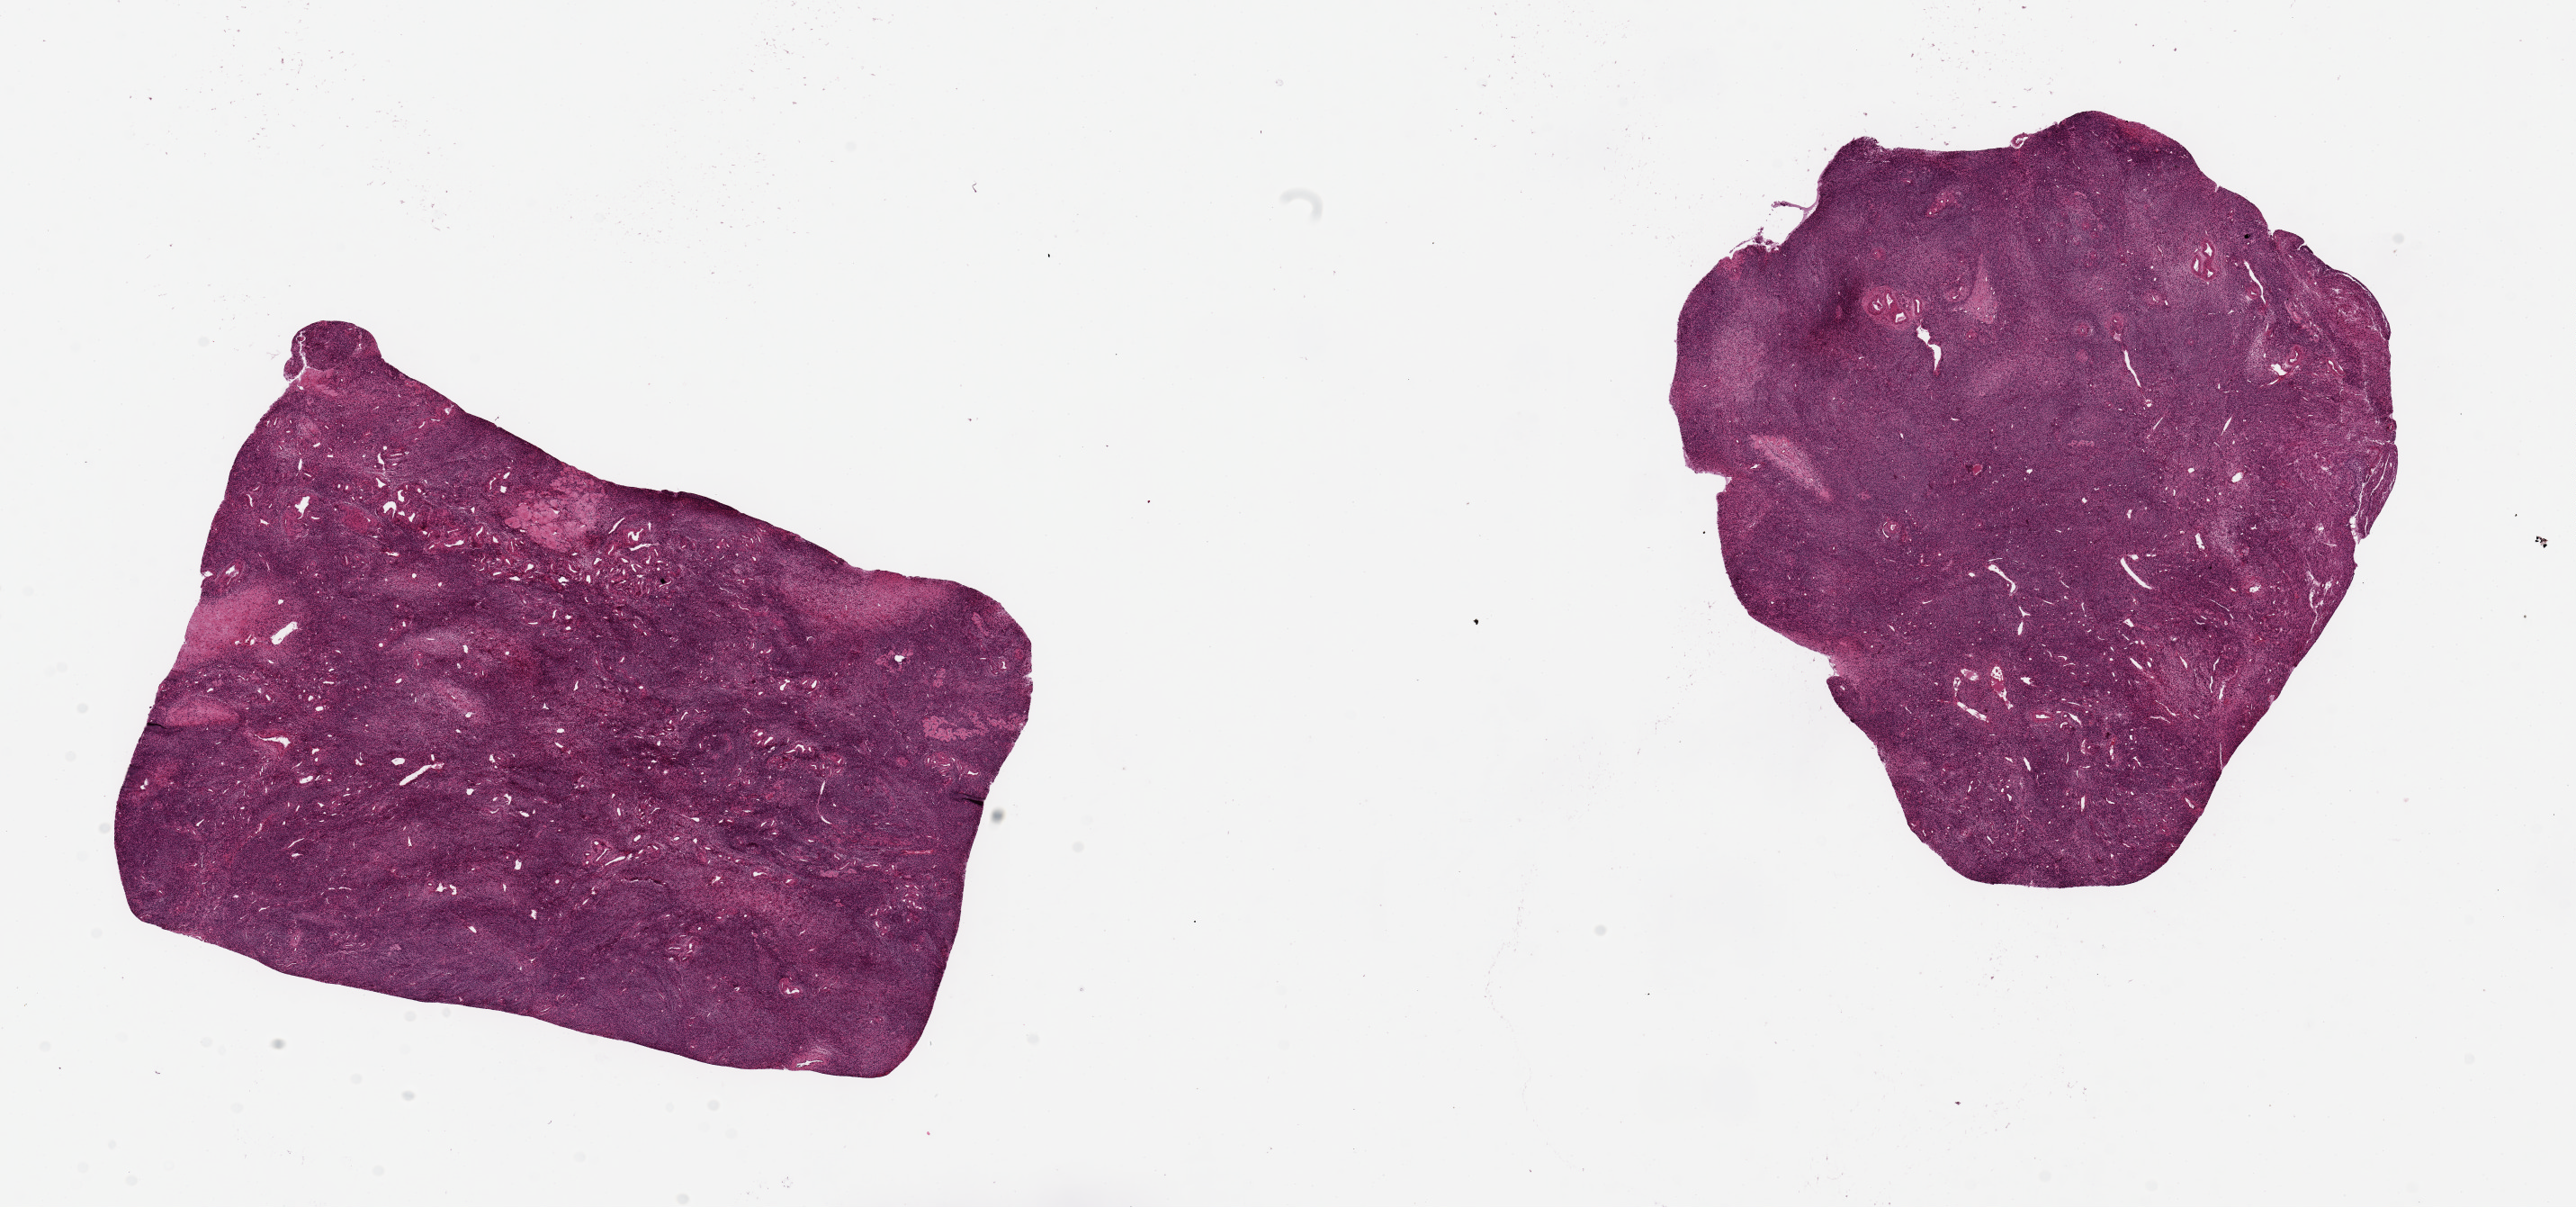
Hematoxylin and eosin (H&E) whole-slide image, brightfield, a low-resolution overview of the entire scanned area, about 22.6 x 10.6 mm (slide scanned at 20x), PAXgene-fixed paraffin-embedded (PFPE) section, section of ovary (target tissue), tissue donor sample. Donor: female.
Reviewer comment on this tissue sample: 2 pieces ovary not fallopian tube, may be used once label corrected.